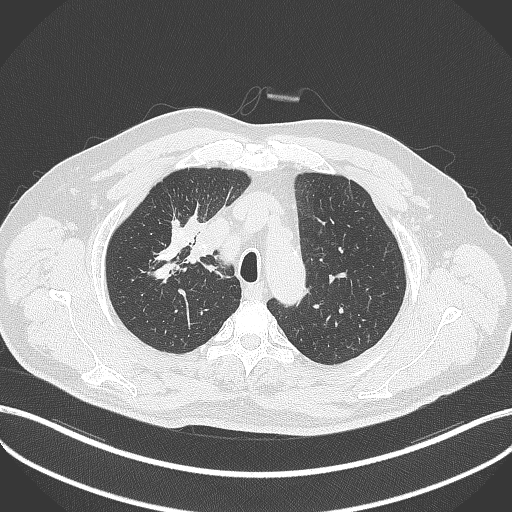
Chest CT, one axial slice. Slice 309 of 411 in the series (ordered by position). Reconstruction kernel B70f. Lung window (W 1500 / L -600 HU). 512 × 512 image matrix. Male patient, age 60 years. Case-level facts recorded for this patient, not image findings: clinical TNM (as recorded): T1b N1 M0.
Annotated regions visible in this slice (bounding box drawn by a radiologist):
- lung tumour (recorded histology: squamous cell carcinoma): bounding box [x1, y1, x2, y2] px = [186, 244, 208, 265]